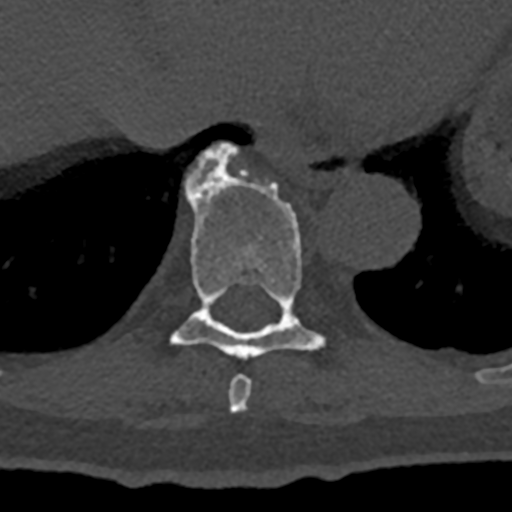
CT including the spine, one axial slice. Position 656 of 797 along the scan axis. Bone window (W 1800 / L 400 HU). 0.5 mm slice thickness. 512 × 512 image matrix, field of view 160 × 160 mm. Patient: male, 74 years. Case-level facts recorded for this patient, not image findings: primary cancer: renal.
Annotated regions visible in this slice (semi-automatic segmentation, software-assisted and operator-edited):
- T10 vertebra: box from (x=199, y=142) to (x=239, y=159) px
- T8 vertebra: (x=228, y=375)–(x=252, y=413)
- T9 vertebra: (x=172, y=145)–(x=324, y=359)